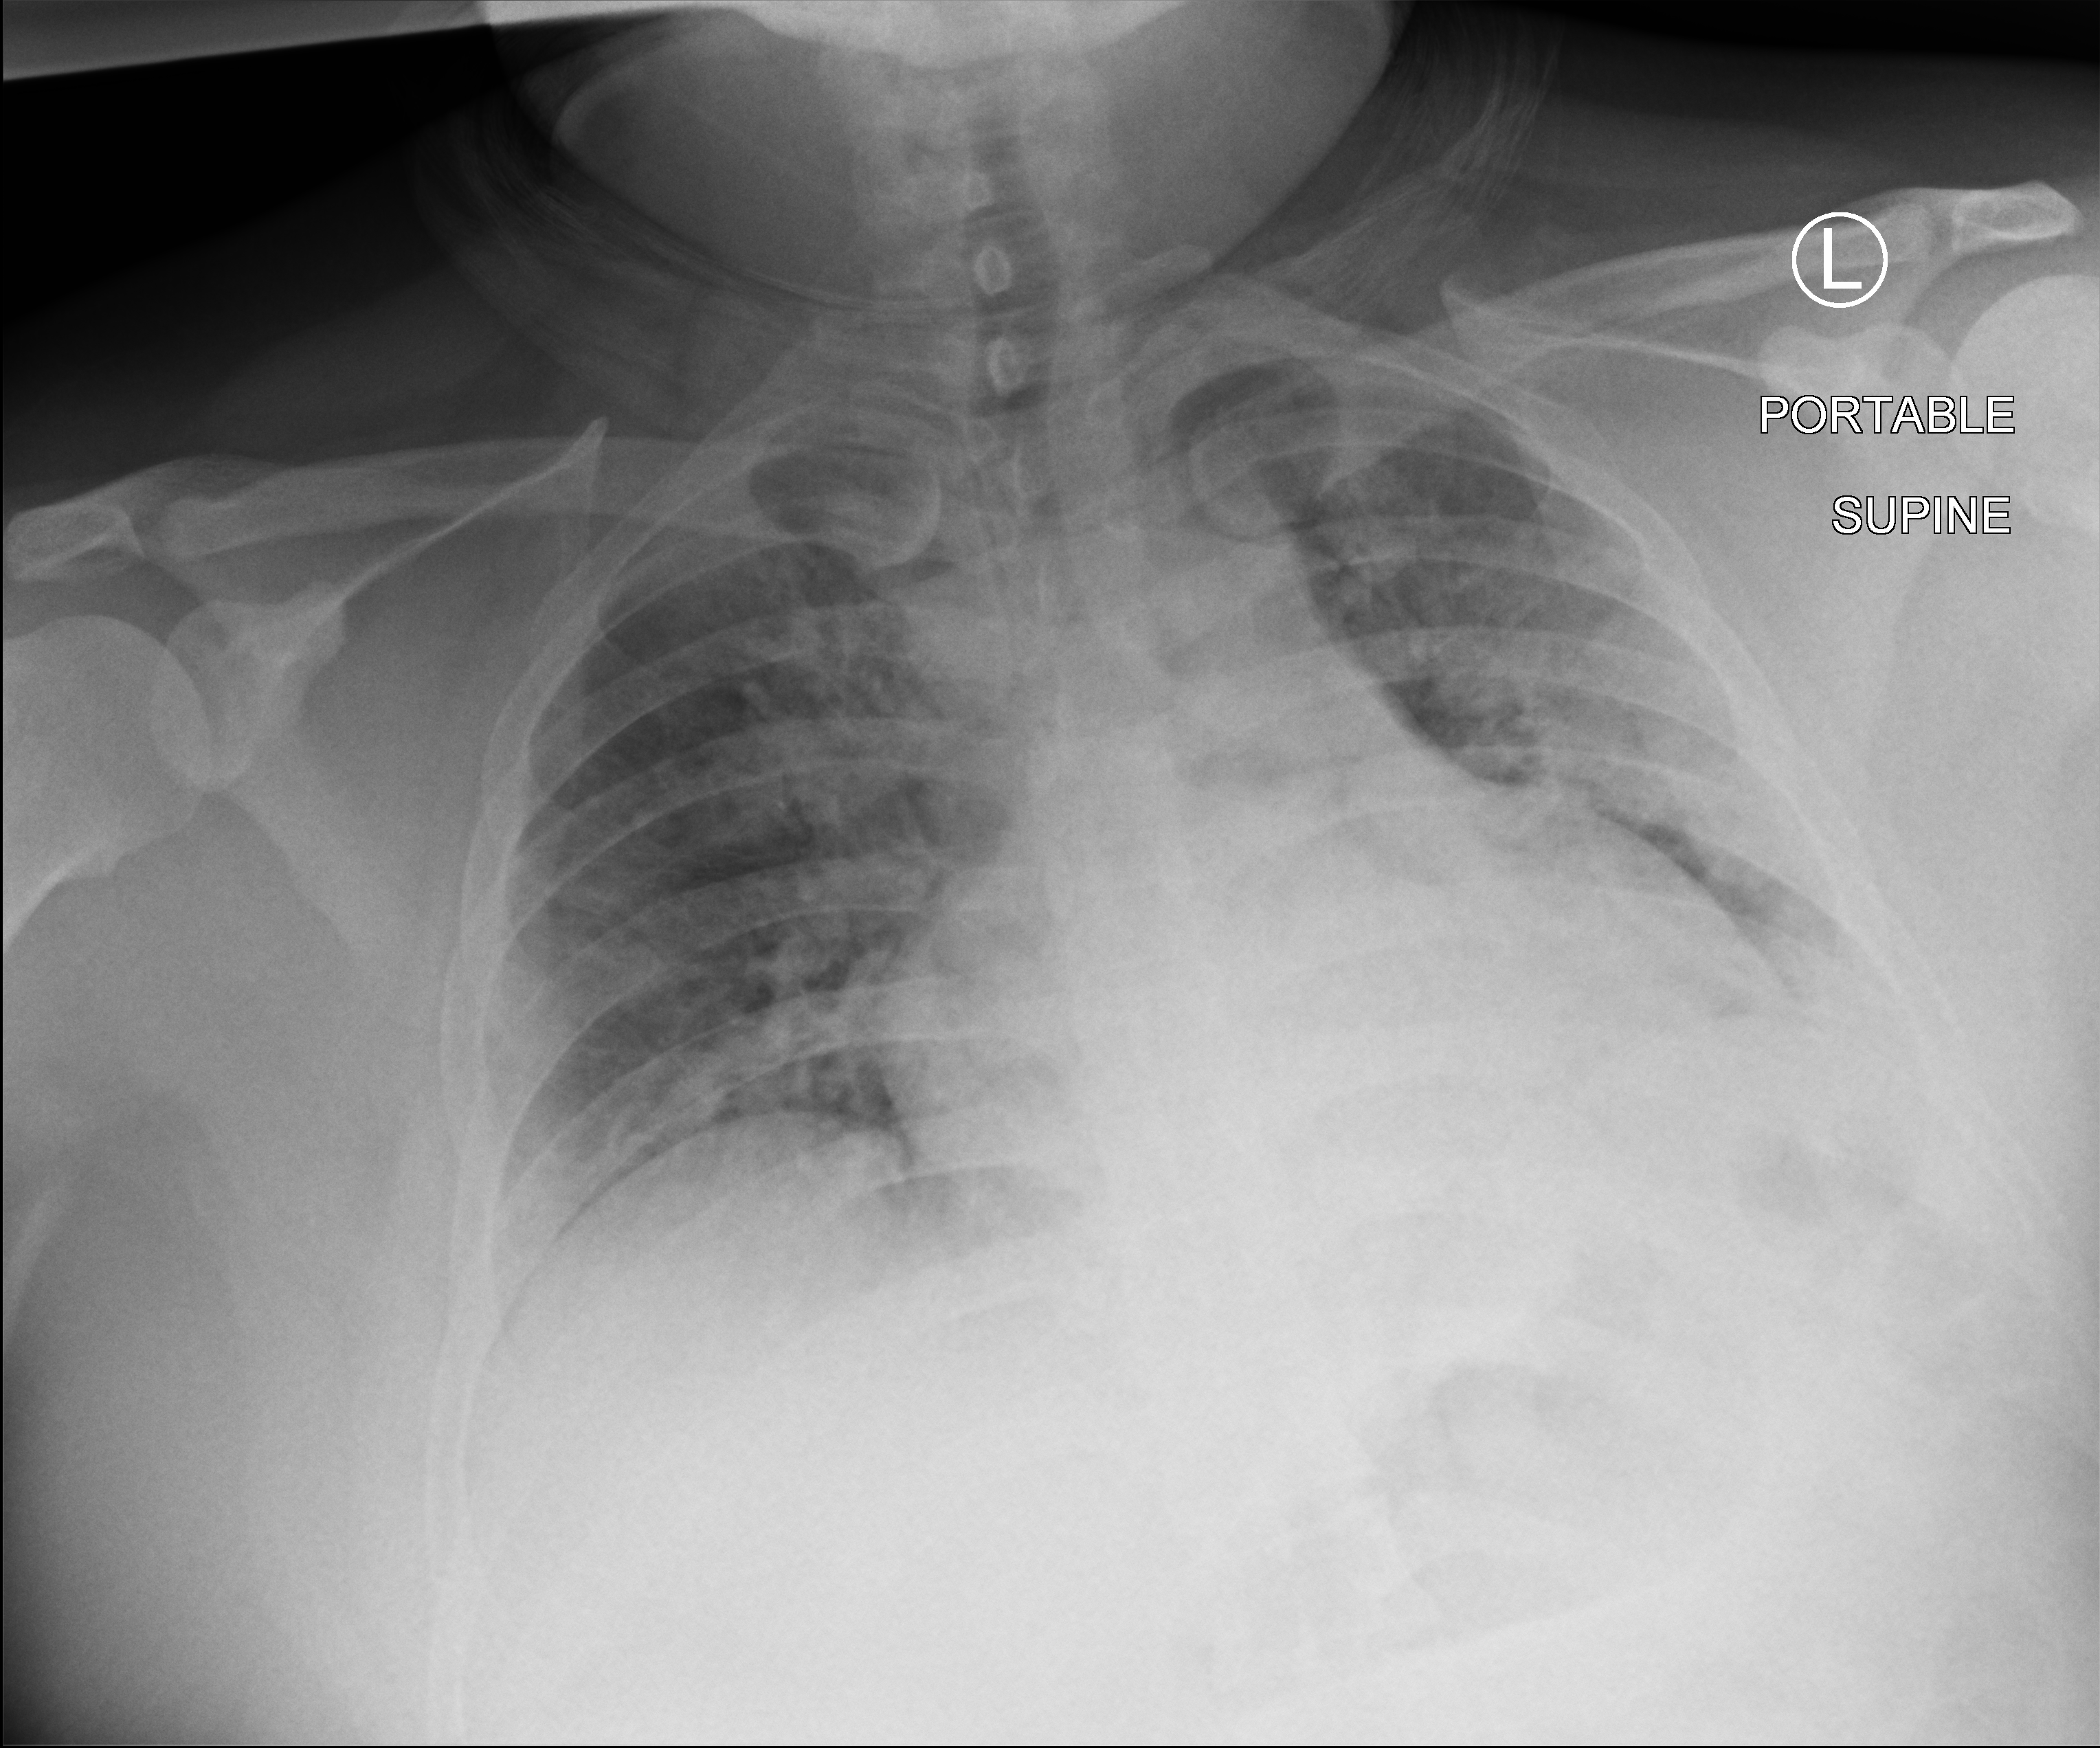
Portable chest radiograph, anteroposterior (AP) projection. Patient hospitalised with COVID-19; male, aged 18–59 years.
From the hospital-stay record, not from the radiograph (when in the stay this image was taken is not recorded):
- mechanically ventilated during this hospital stay: no